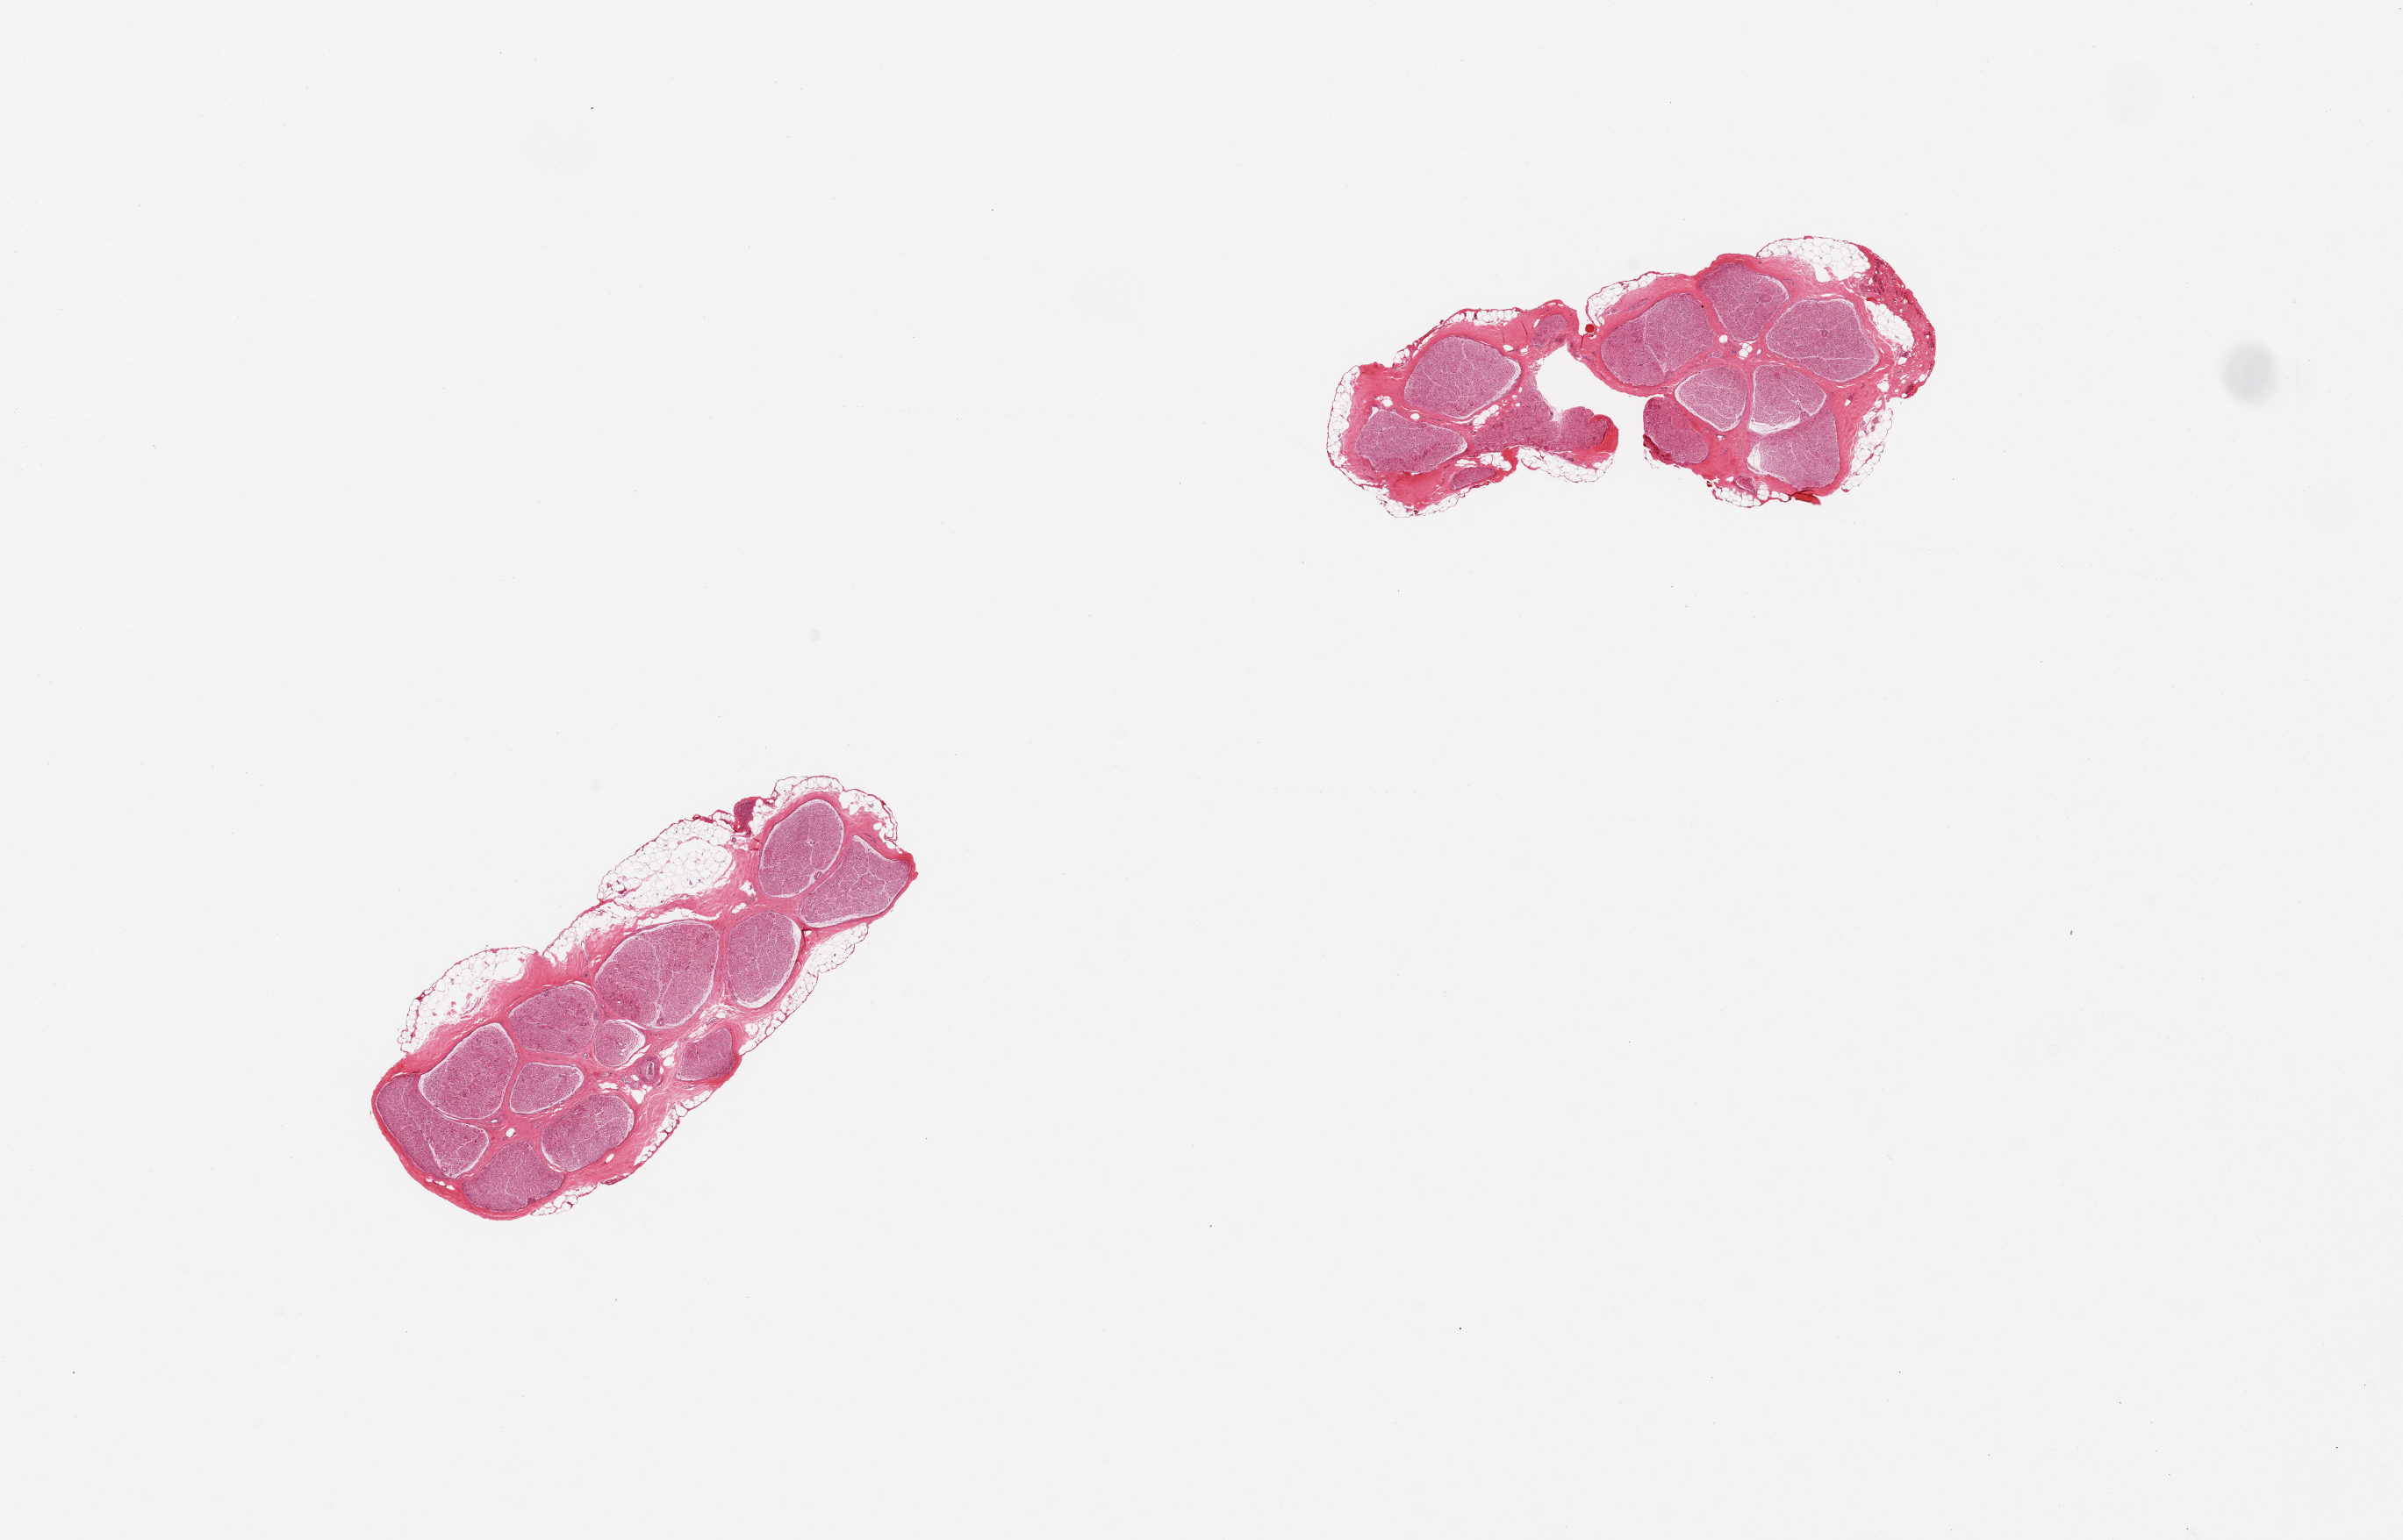
Whole-slide image, H&E stain, whole scanned area (about 21.7 x 13.9 mm, acquisition: 20x scan) shown as a low-resolution overview. PAXgene-fixed, paraffin-embedded tissue. Section of tibial nerve (target tissue). Tissue donor sample. Donor sex: male.
Review note (as recorded): 2 pieces, fairly good specimens, discontinuous adherent rims of fat, up to ~0.5mm.